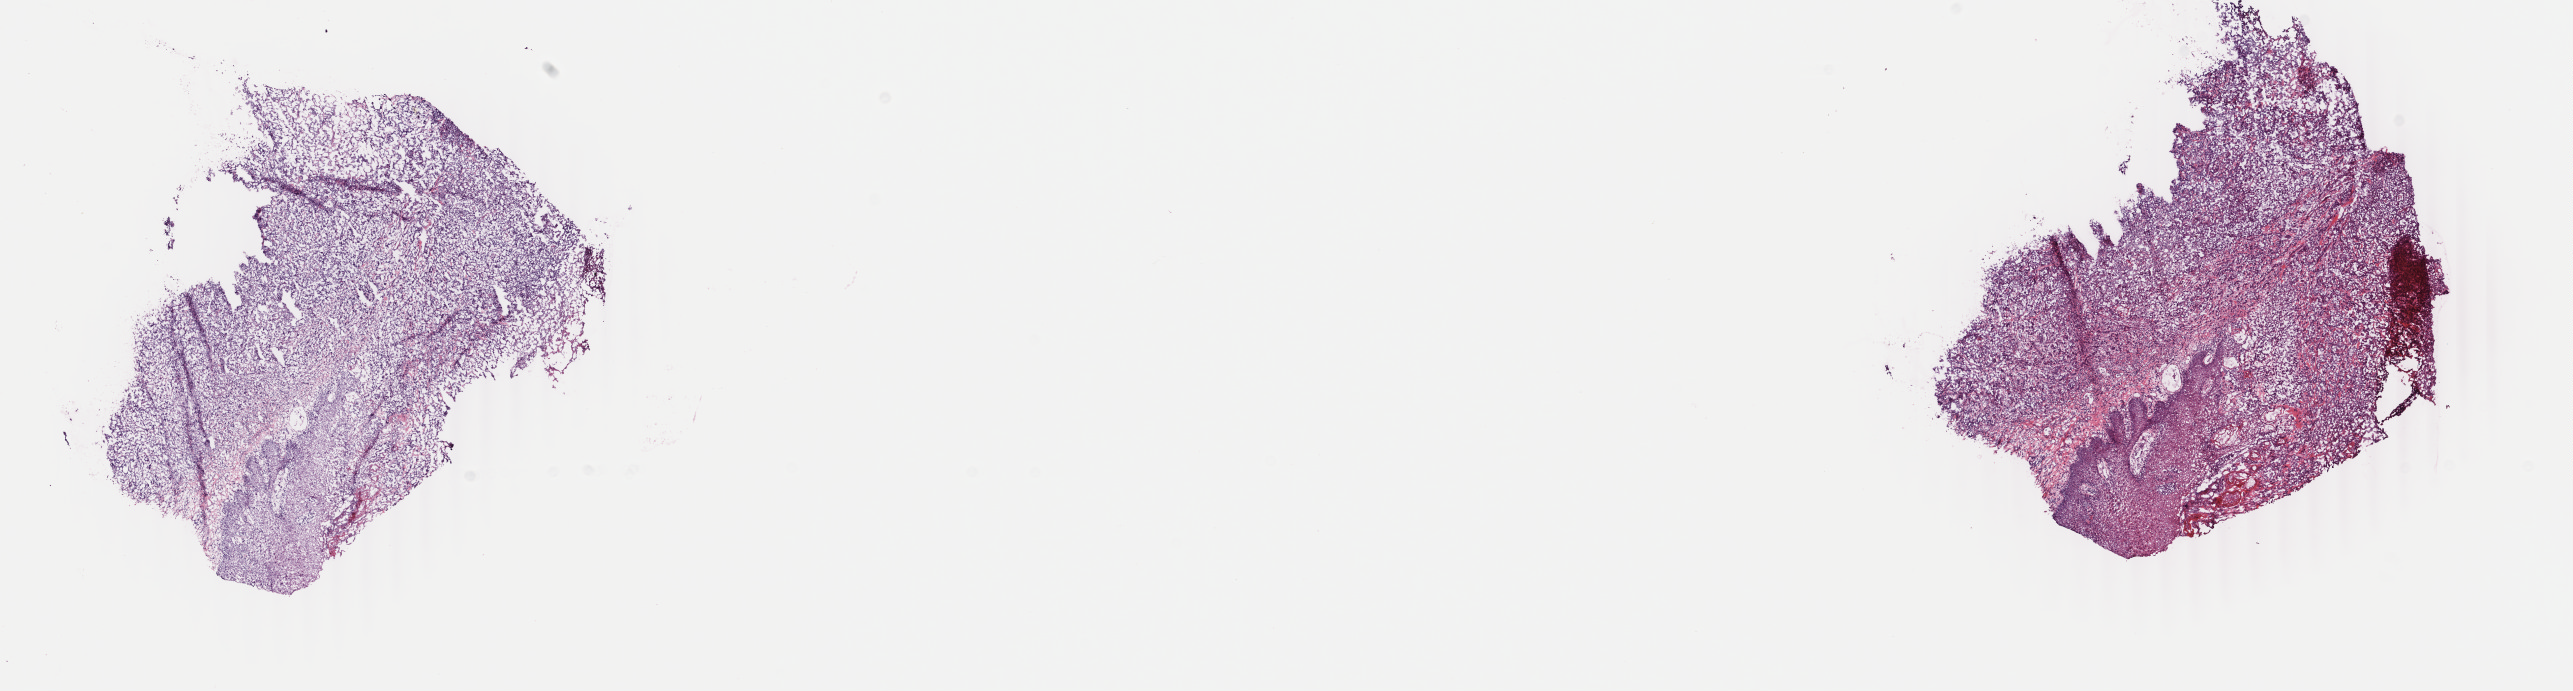
Whole-slide histology image, Hematoxylin and eosin (H&E) stained — low-resolution overview of the scanned area, about 20.5 x 5.5 mm; frozen section from the top of the tissue portion; sample: primary tumour, head and neck. Female patient; age at initial diagnosis 62 years. Histologic grade: G2 (moderately differentiated). Pathologist review of this section (percent, as recorded): tumour cells 80%, tumour nuclei 80%, normal cells 0%, stromal cells 10%, necrosis 10%. Inflammatory infiltration, as recorded: lymphocyte infiltration 40%, monocyte infiltration 20%, neutrophil infiltration 20%.
- lymph nodes positive (case pathology): 5 of 28 examined
- pathologic diagnosis: Squamous cell carcinoma, NOS (hypopharynx, NOS)
- AJCC pathologic stage: IVA (7th edition)